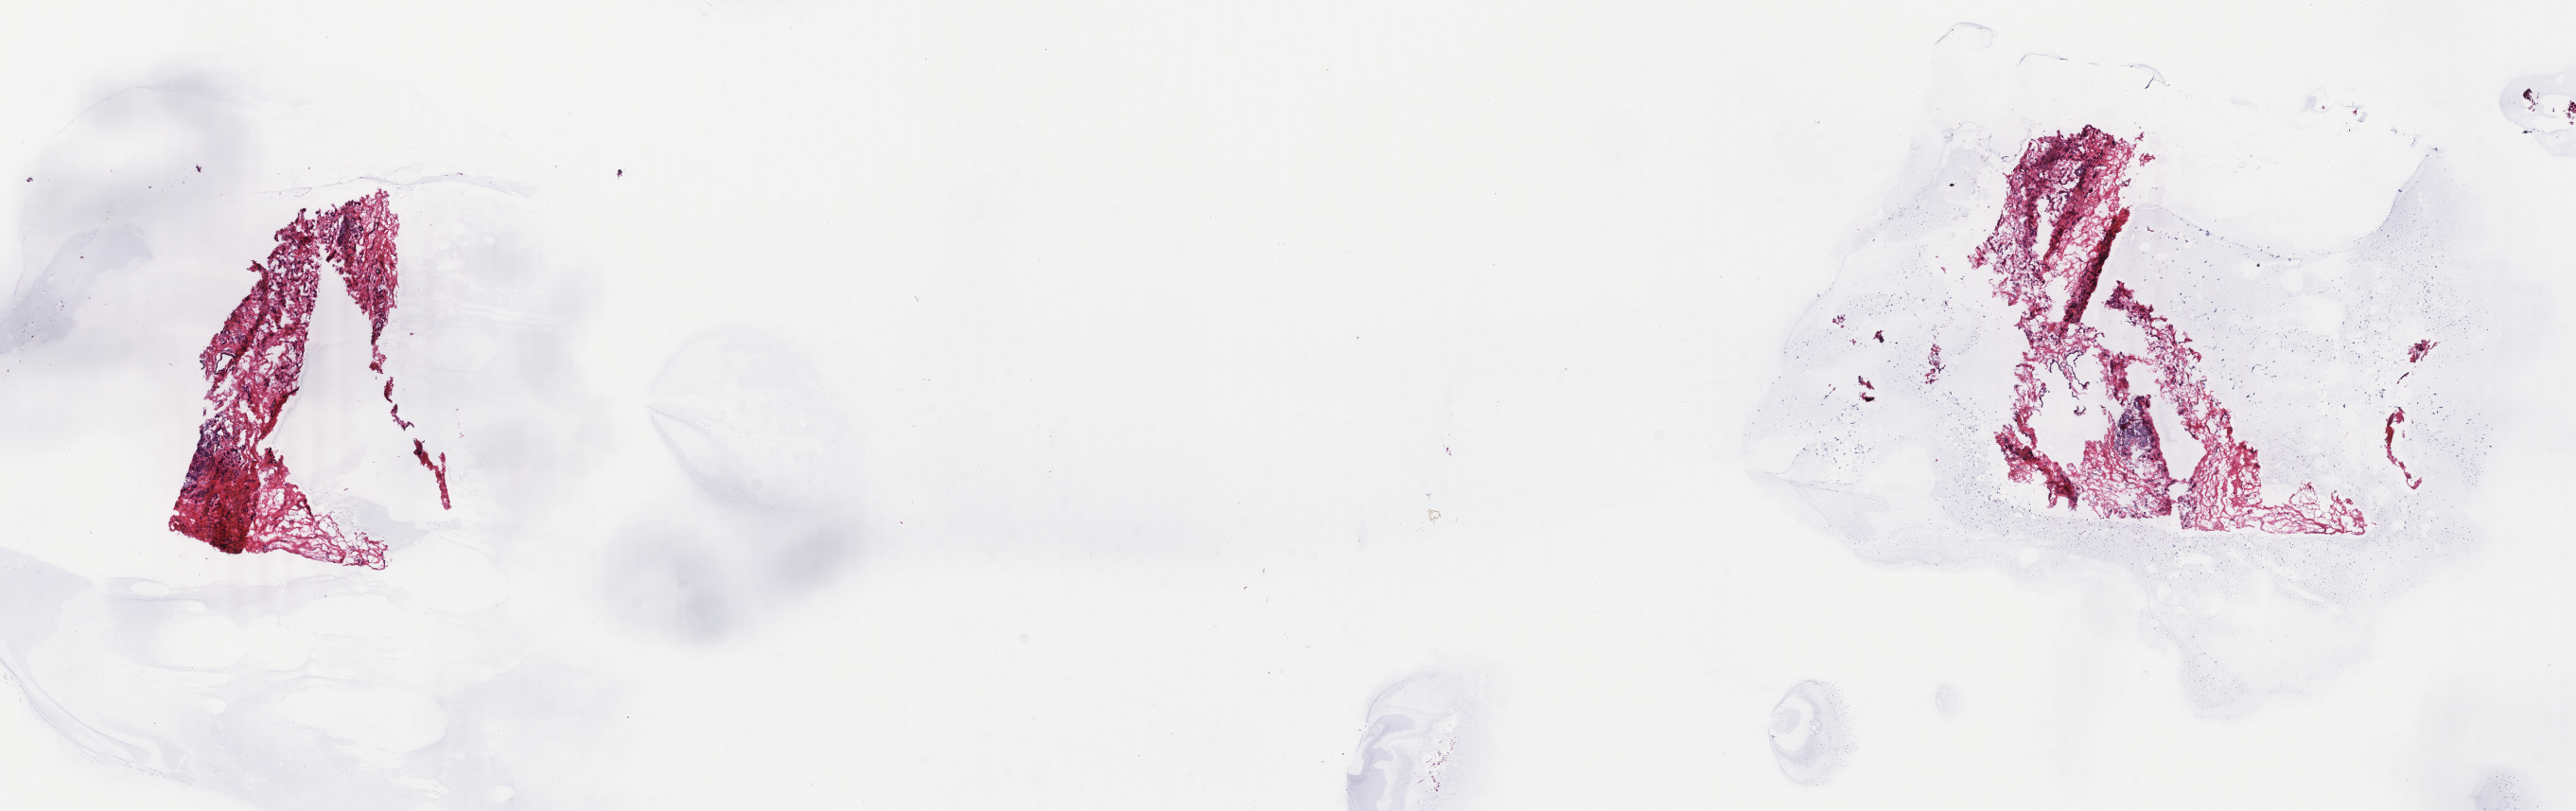
Whole-slide histology image, H&E, whole scanned area (about 21.7 x 6.8 mm, slide scanned at 40x) shown as a low-resolution overview; frozen section from the top of the tissue portion; sample: primary tumour, breast. Patient: female, age at initial diagnosis 50 years. Pathologist review of this section (percent, as recorded): tumour cells 90%, tumour nuclei 75%, normal cells 0%, stromal cells 10%, necrosis 0%. Inflammatory infiltration, as recorded: lymphocyte infiltration 0%, monocyte infiltration 0%, neutrophil infiltration 0%.
TNM: T2 N2a M0. Pathologic diagnosis: Infiltrating duct carcinoma, NOS. Laterality: right. AJCC pathologic stage: IIIA (7th edition). Lymph nodes positive (case pathology): 4 of 9 examined.